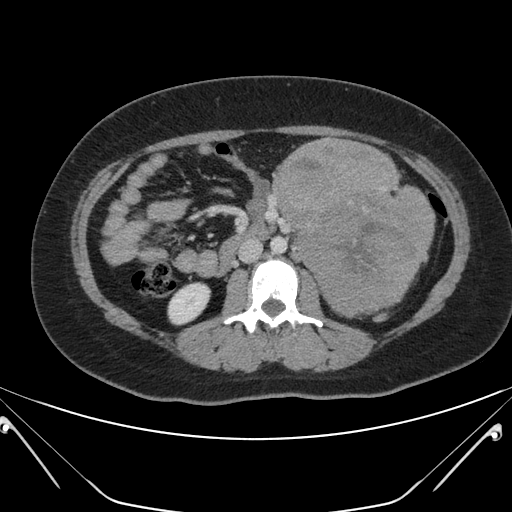
Contrast-enhanced abdominal CT, one axial slice. Slice 101 of 168 in the series (ordered by position). 120 kVp. Intravenous contrast given. Soft-tissue window (W 400 / L 40 HU). 3 mm slice thickness. 512 × 512 image matrix, field of view 394 × 394 mm. Female patient, age 26 years. From the clinical record (not read from this slice): diagnosis: adrenocortical carcinoma; tumour side: left adrenal; tumour size at pathology: 28 cm; Ki-67 index: 20 %; stage (as recorded): 2.
Structures marked on this image (semi-automatic segmentation, software-assisted and operator-edited):
- mass: bounding box <277,140,433,315> (left, top, right, bottom; pixels)